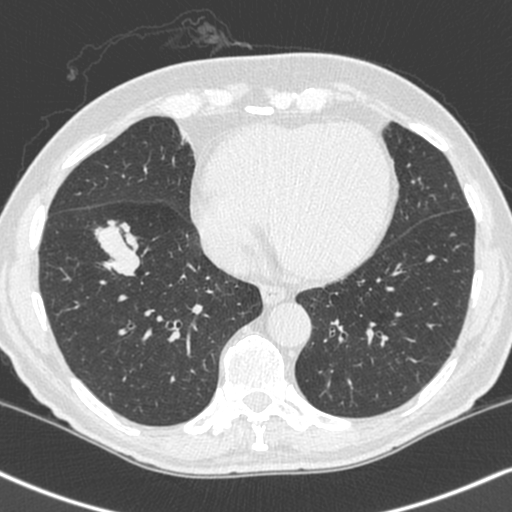
Axial slice from a low-dose chest CT screening exam. Baseline screening round. Lung window (W 1500 / L -600 HU). Standard (soft-tissue) reconstruction kernel (C). Slice 154 of 248 in the series. 512 × 512 image matrix. Male participant, aged 68 years at enrolment.
Expert-annotated lung lesion, bounding box (x1, y1, x2, y2) in pixels: (81, 210, 156, 280). Screening reader's record for this exam (one nodule recorded; not confirmed to be the boxed lesion): non-calcified nodule or mass ≥4 mm, right lower lobe, 34 × 17 mm, smooth margins, soft tissue attenuation. Lung cancer was diagnosed 24 days after this screen: combined small cell carcinoma, right lower lobe, stage IIIA (AJCC 6th edition), 41 mm at pathology.